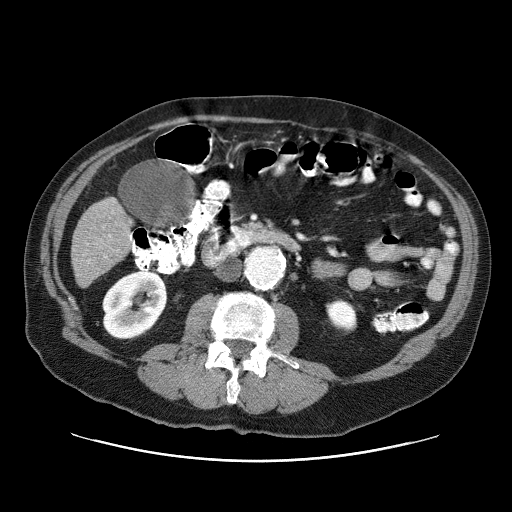
Contrast-enhanced abdominal CT (liver protocol), one axial slice; position 10 of 87 along the scan axis; reconstruction kernel STANDARD; 120 kVp; one of 3 acquisitions stored at this slice position; soft-tissue window (W 400 / L 40 HU); 2.5 mm slice thickness; 512 × 512 image matrix. From the clinical record (not read from this slice): diagnosis: hepatocellular carcinoma (patient treated with transarterial chemoembolisation; whether this scan precedes or follows treatment is not stated here); TNM stage (as recorded): Stage-IIIA; Child-Pugh class: A; tumour nodularity: multinodular; tumour size: 6 cm.
Structures marked on this image (semi-automatically segmented with operator editing):
- liver parenchyma outside the tumour (the mass and vessels are separate outlines, so this box may not span the whole liver): bounding box <70,198,132,287> (left, top, right, bottom; pixels)
- liver vessels: <129,235,132,239>